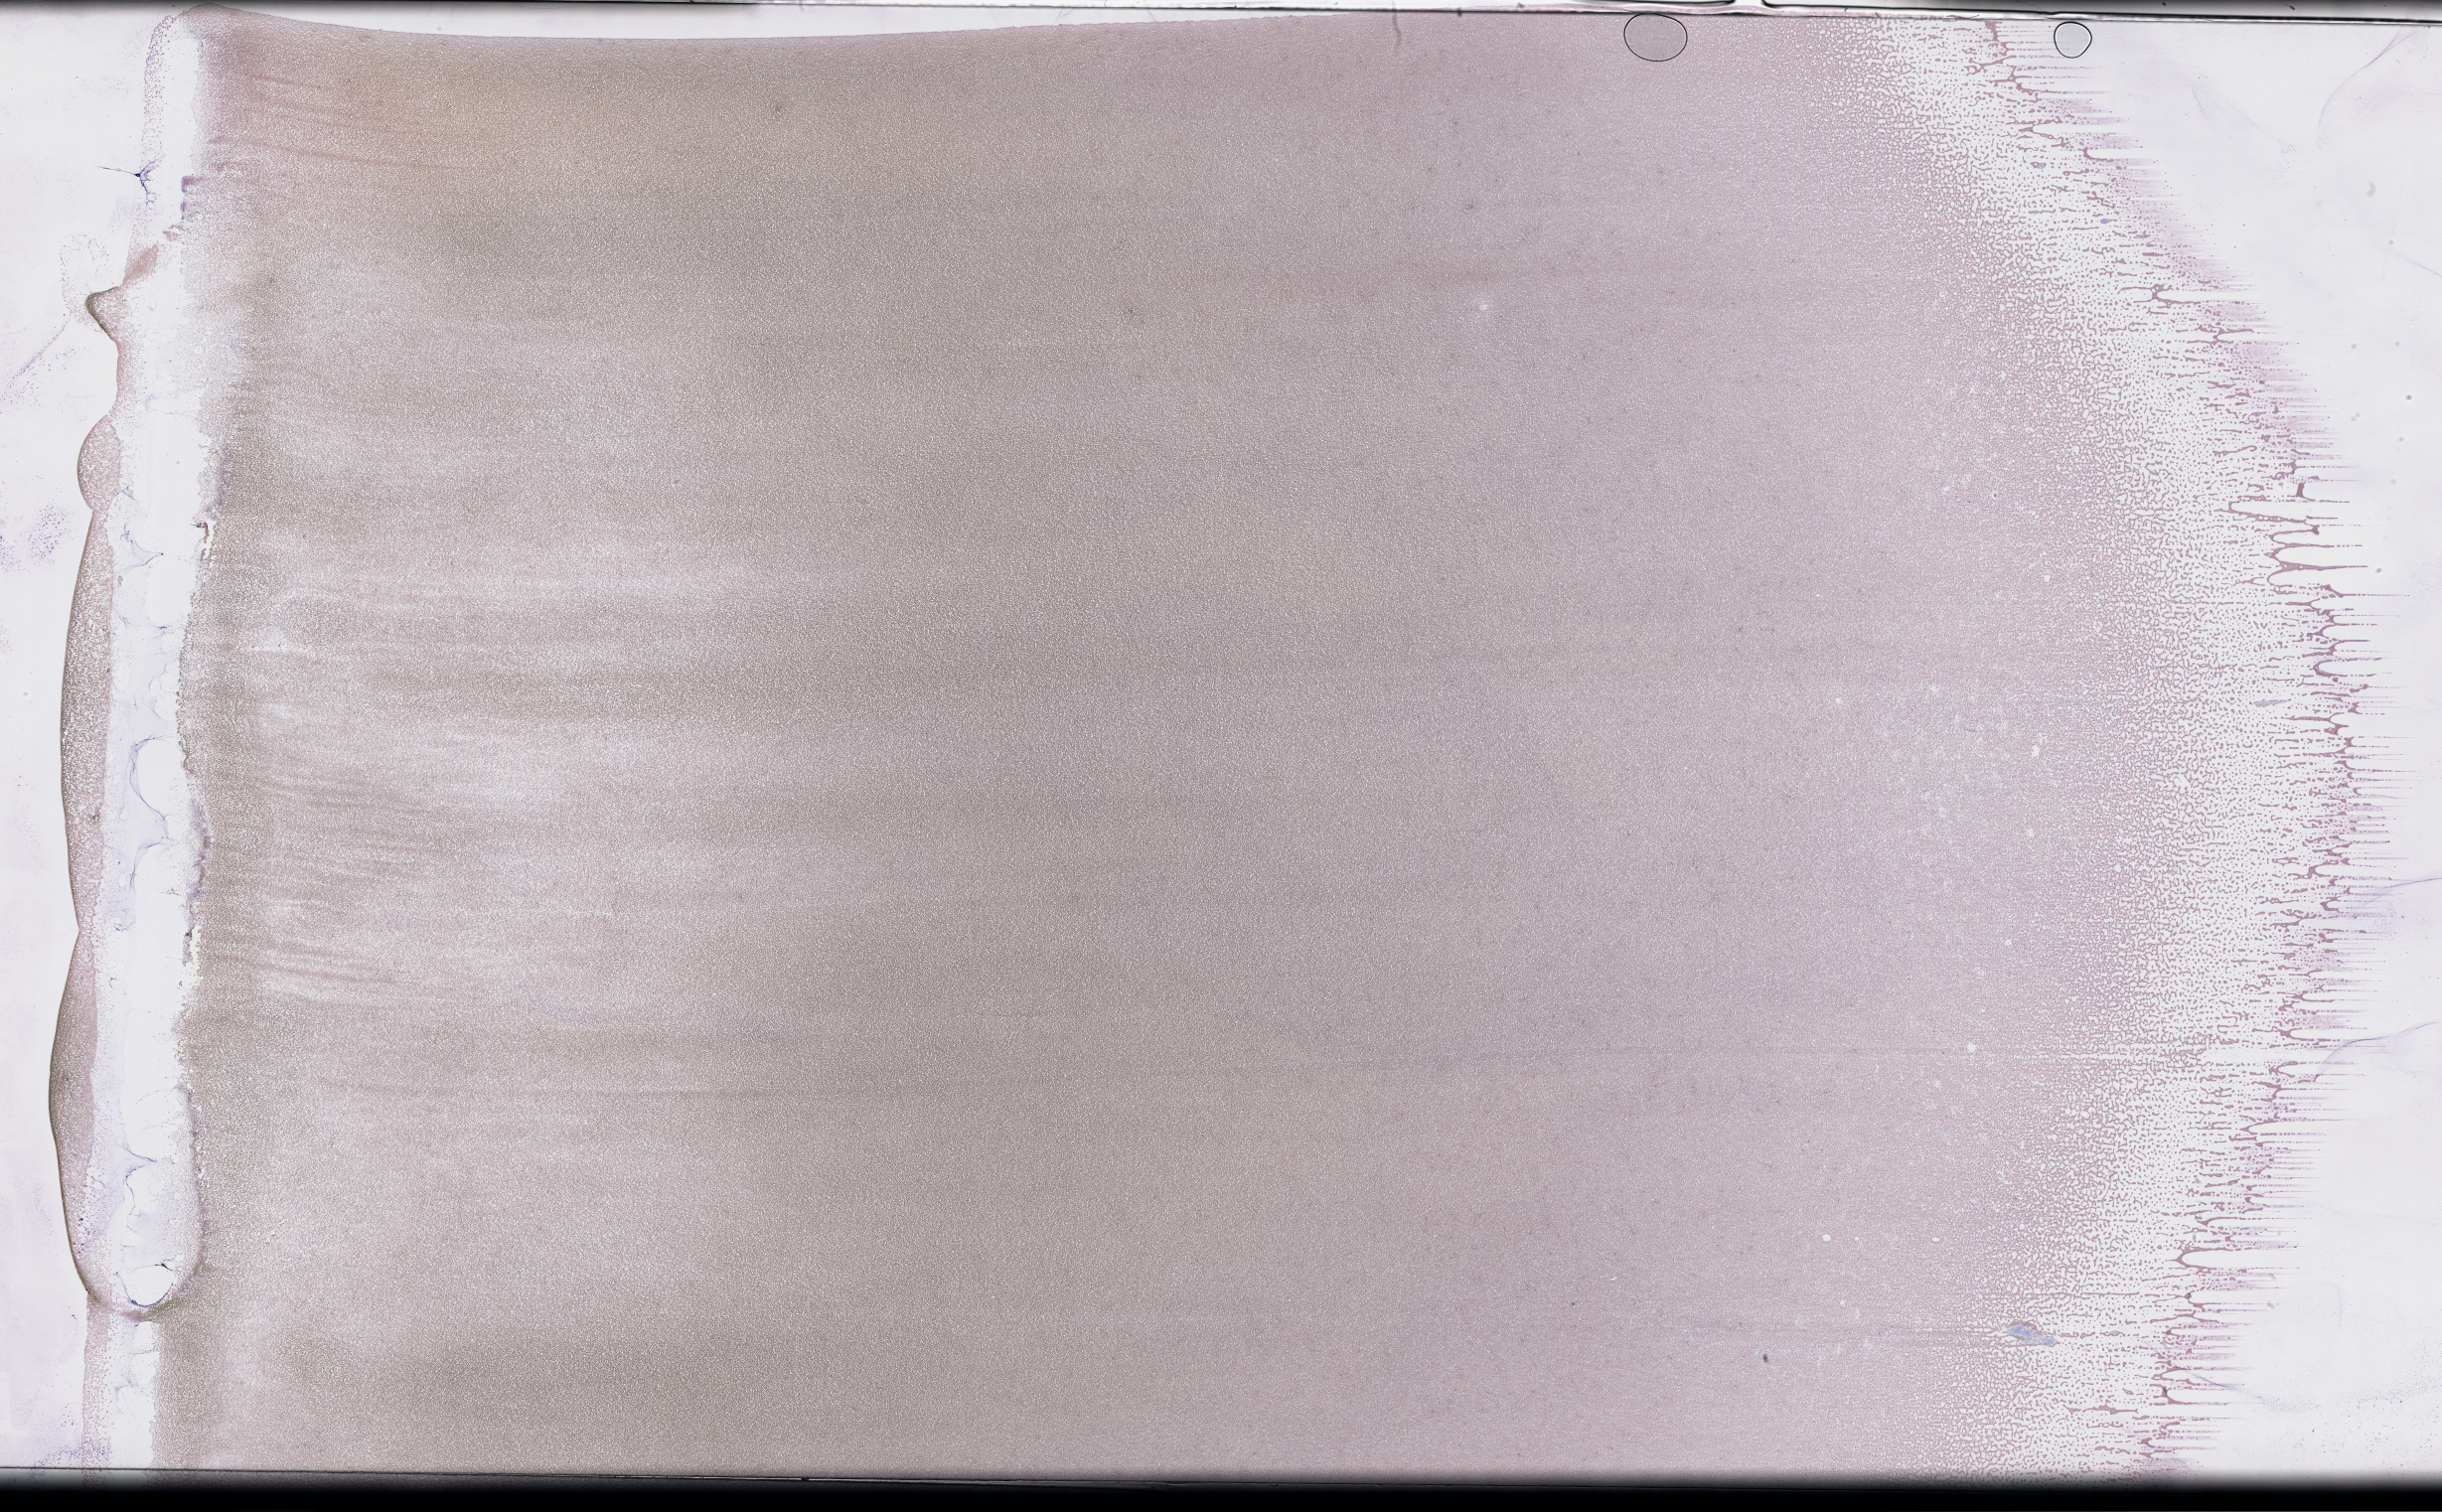
Whole-slide image of a whole blood smear, Wright–Giemsa stain — low-resolution overview of the scanned area, about 39.7 x 24.6 mm. Smear from an EDTA sample. Specimen time point: collected on treatment. Patient: male.
From a patient with: Plasma Cell Myeloma.